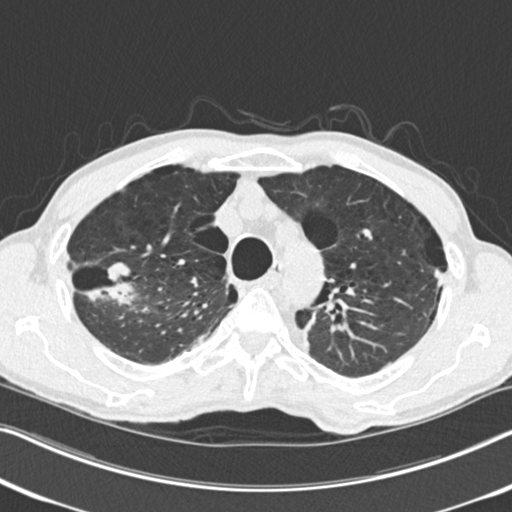
Low-dose screening chest CT, one axial slice; slice 193 of 251 in the series (ordered by position); reconstruction kernel B30f; lung window (W 1500 / L -600 HU); 512 × 512 image matrix.
Outlined on this slice (manually delineated by an expert):
- lesion 1 (tumor, upper lobe of right lung): bounding box [x1, y1, x2, y2] px = [87, 263, 137, 303]